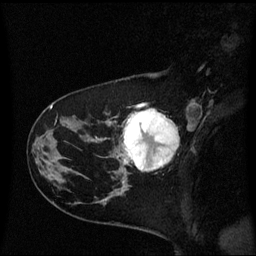
Breast MRI (dynamic contrast-enhanced), one sagittal slice. Position 19 of 60 along the scan axis. Dynamic contrast-enhanced series, image 2 of 3 at this slice position (ordered by acquisition). 1.5 T. TE 4.2 ms, TR 8.4 ms. 2 mm slice thickness. 256 × 256 image matrix, field of view 220 × 220 mm. Female patient, age 41 years. From the clinical record (not read from this slice): setting: breast cancer imaged before/during neoadjuvant chemotherapy; receptor status: triple-negative.
Outlined on this slice (semi-automatically segmented with operator editing):
- analysis volume of interest (the breast-tissue region the enhancement analysis was run in; not a lesion): bounding box [x1, y1, x2, y2] px = [116, 108, 179, 177]
- tumour enhancement mask (voxels above the 70 % enhancement threshold inside the analysis volume of interest): [123, 110, 179, 171]